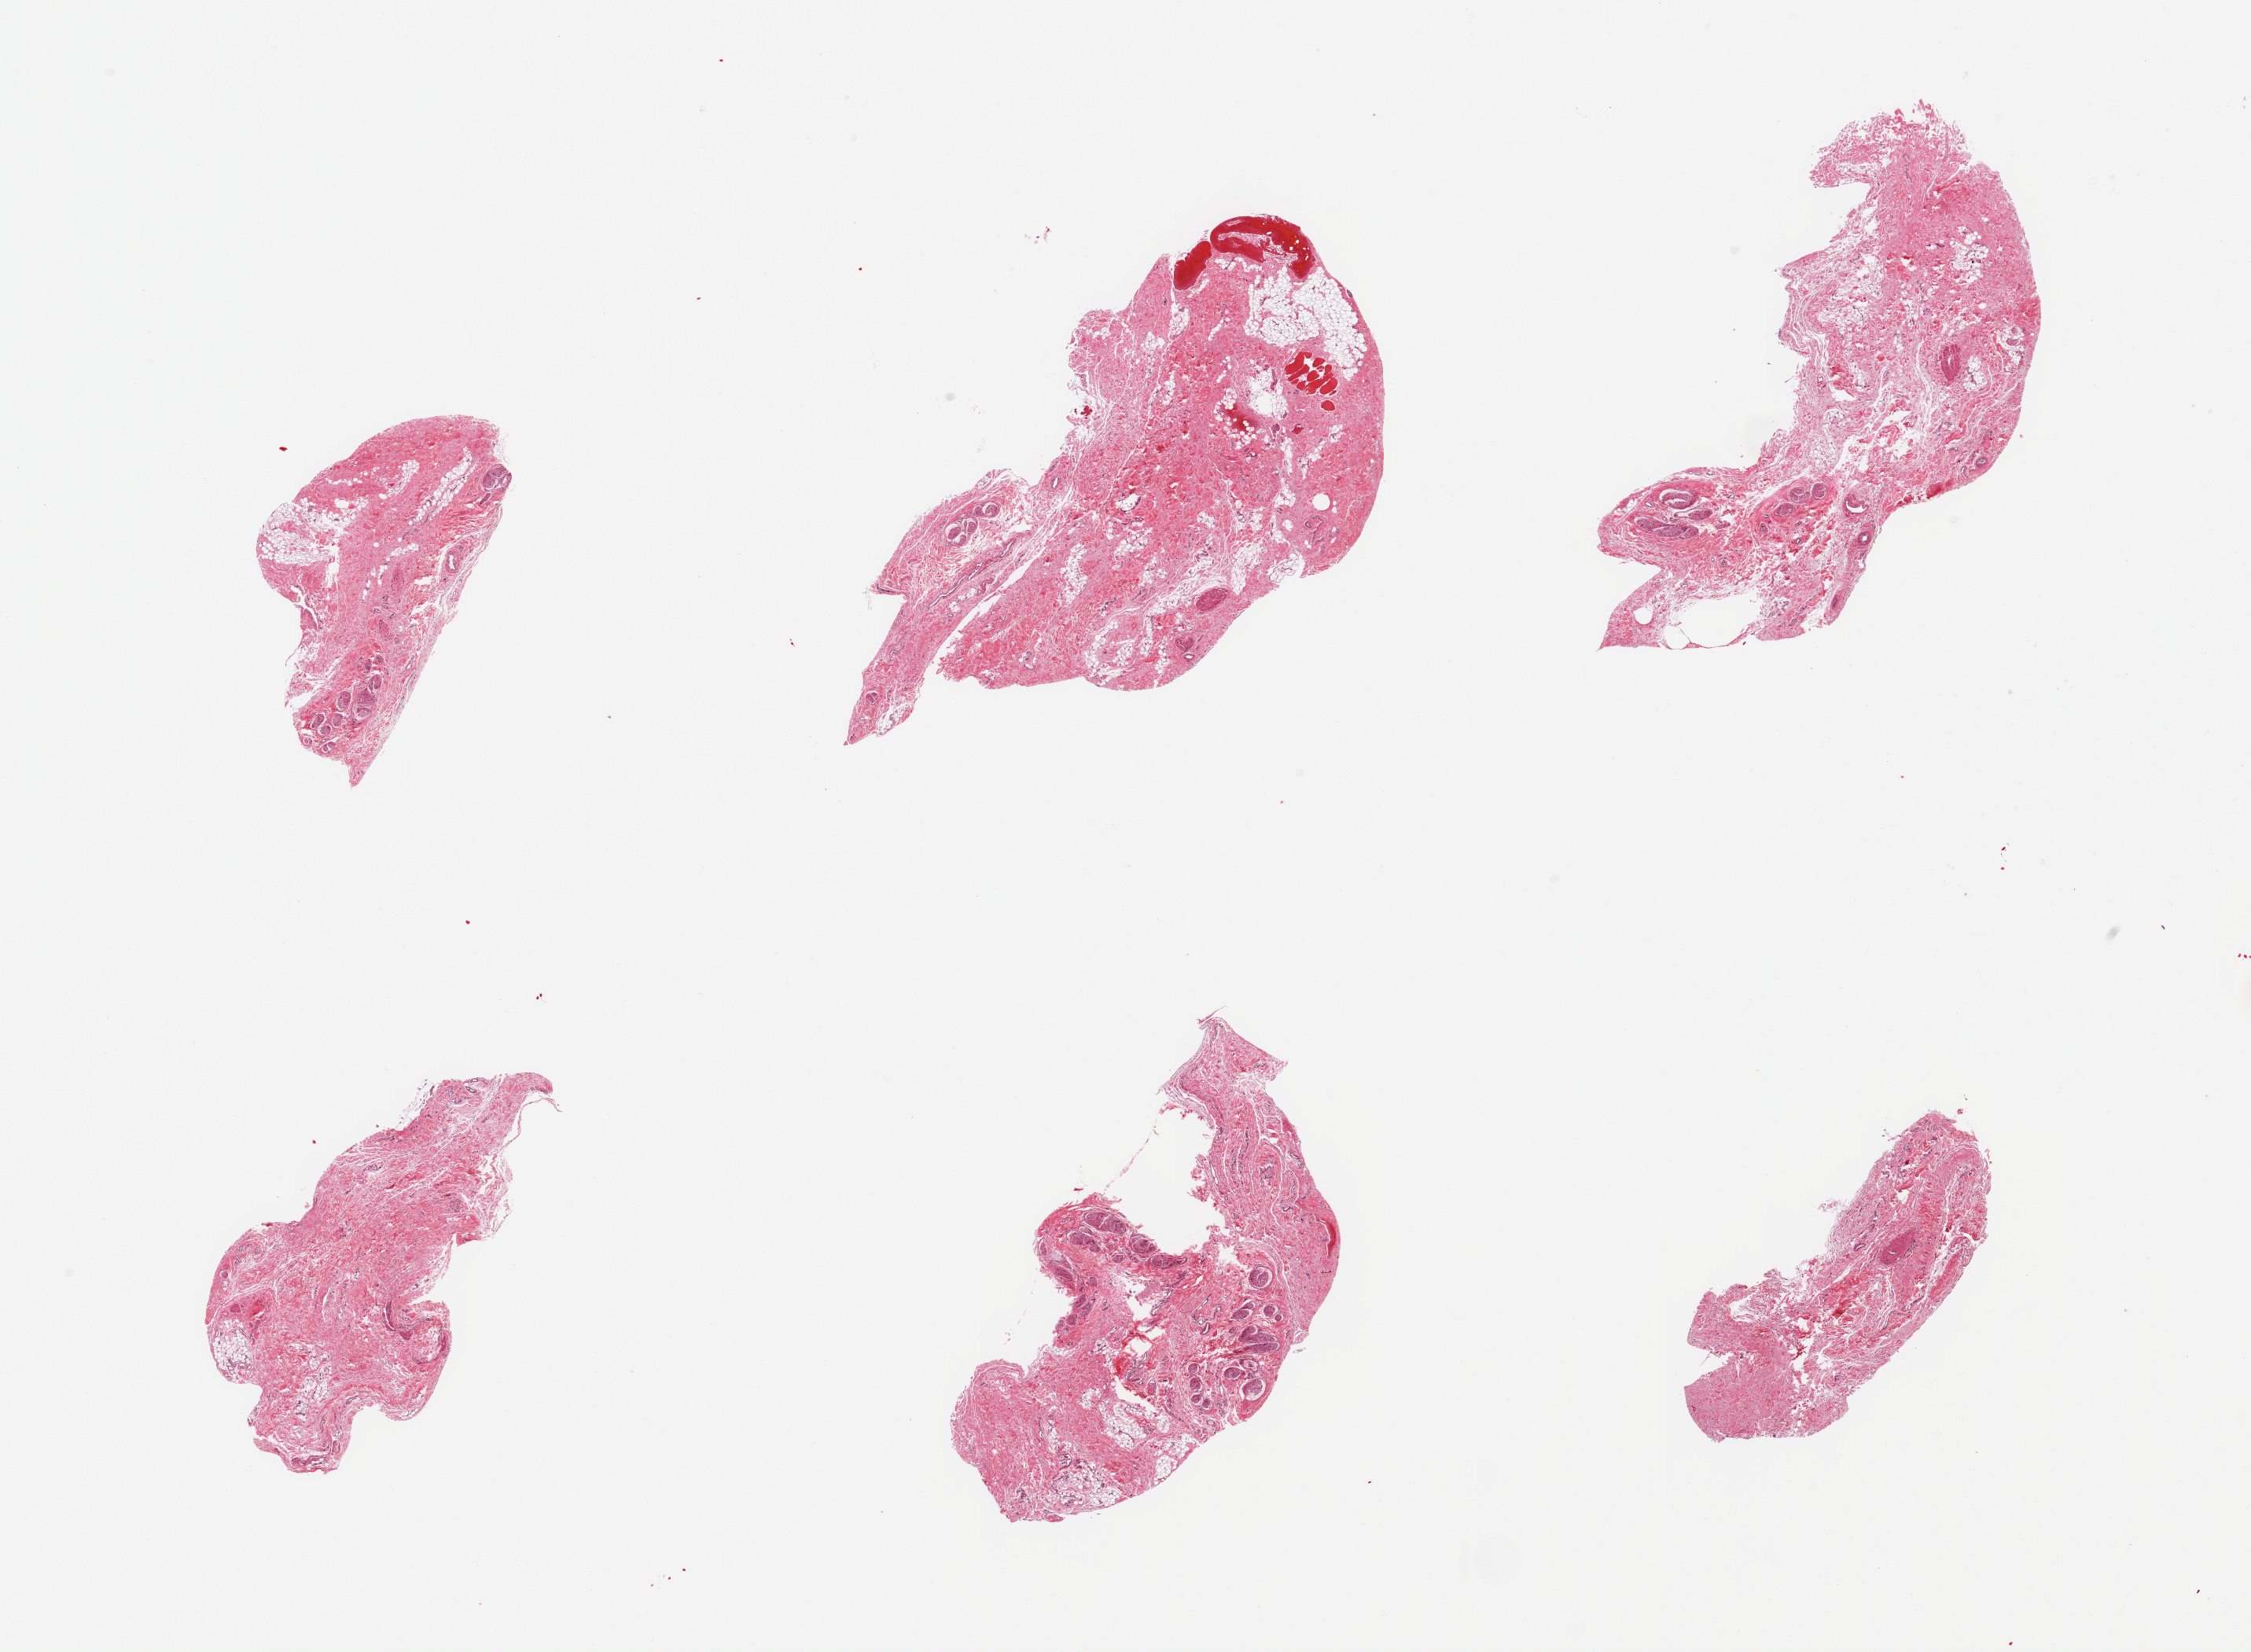
Whole-slide image, haematoxylin and eosin stain, brightfield — shown as a low-resolution overview of the whole scanned area (about 22.6 x 16.6 mm). PAXgene-fixed, paraffin-embedded tissue. Section of esophageal muscle (target tissue). Tissue donor sample. Donor: male.
Review note (as recorded): 6 pieces; submucosa.